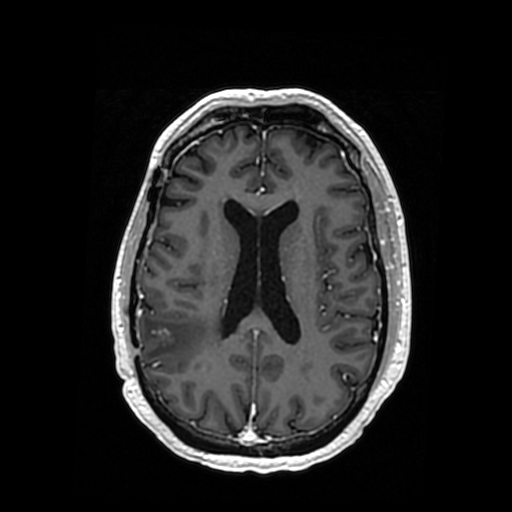
Brain MRI from a brain-tumour surgery series, one axial slice; slice 150 of 364 in the series (ordered by position); T1-weighted post-contrast; 0.5 mm slice thickness; 512 × 512 image matrix. From the clinical record (not read from this slice): histopathology: Oligodendroglioma; WHO grade: 3; IDH mutation: yes; tumour location: Right Posterior Temporal Inferior Parietal.
Outlined on this slice (manually delineated by an expert):
- tumour: bounding box [x1, y1, x2, y2] px = [161, 330, 169, 337]